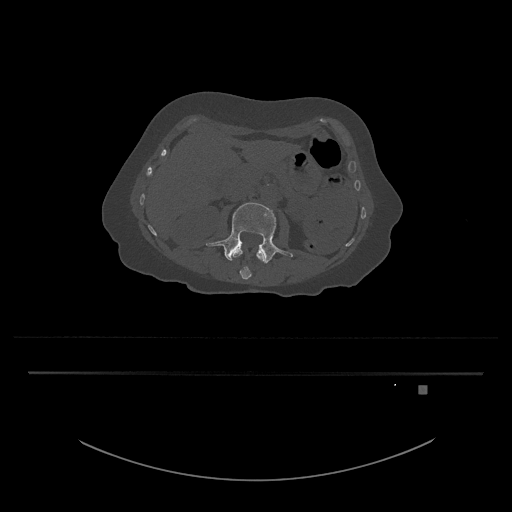
CT including the spine, one axial slice; slice 447 of 797 in the series (ordered by position); 120 kVp; bone window (W 1800 / L 400 HU); 512 × 512 image matrix. Patient: female, 57 years. From the clinical record (not read from this slice): primary cancer: cervical.
Structures marked on this image (semi-automatic segmentation, software-assisted and operator-edited):
- L3 vertebra: bounding box [x1, y1, x2, y2] px = [206, 202, 293, 264]